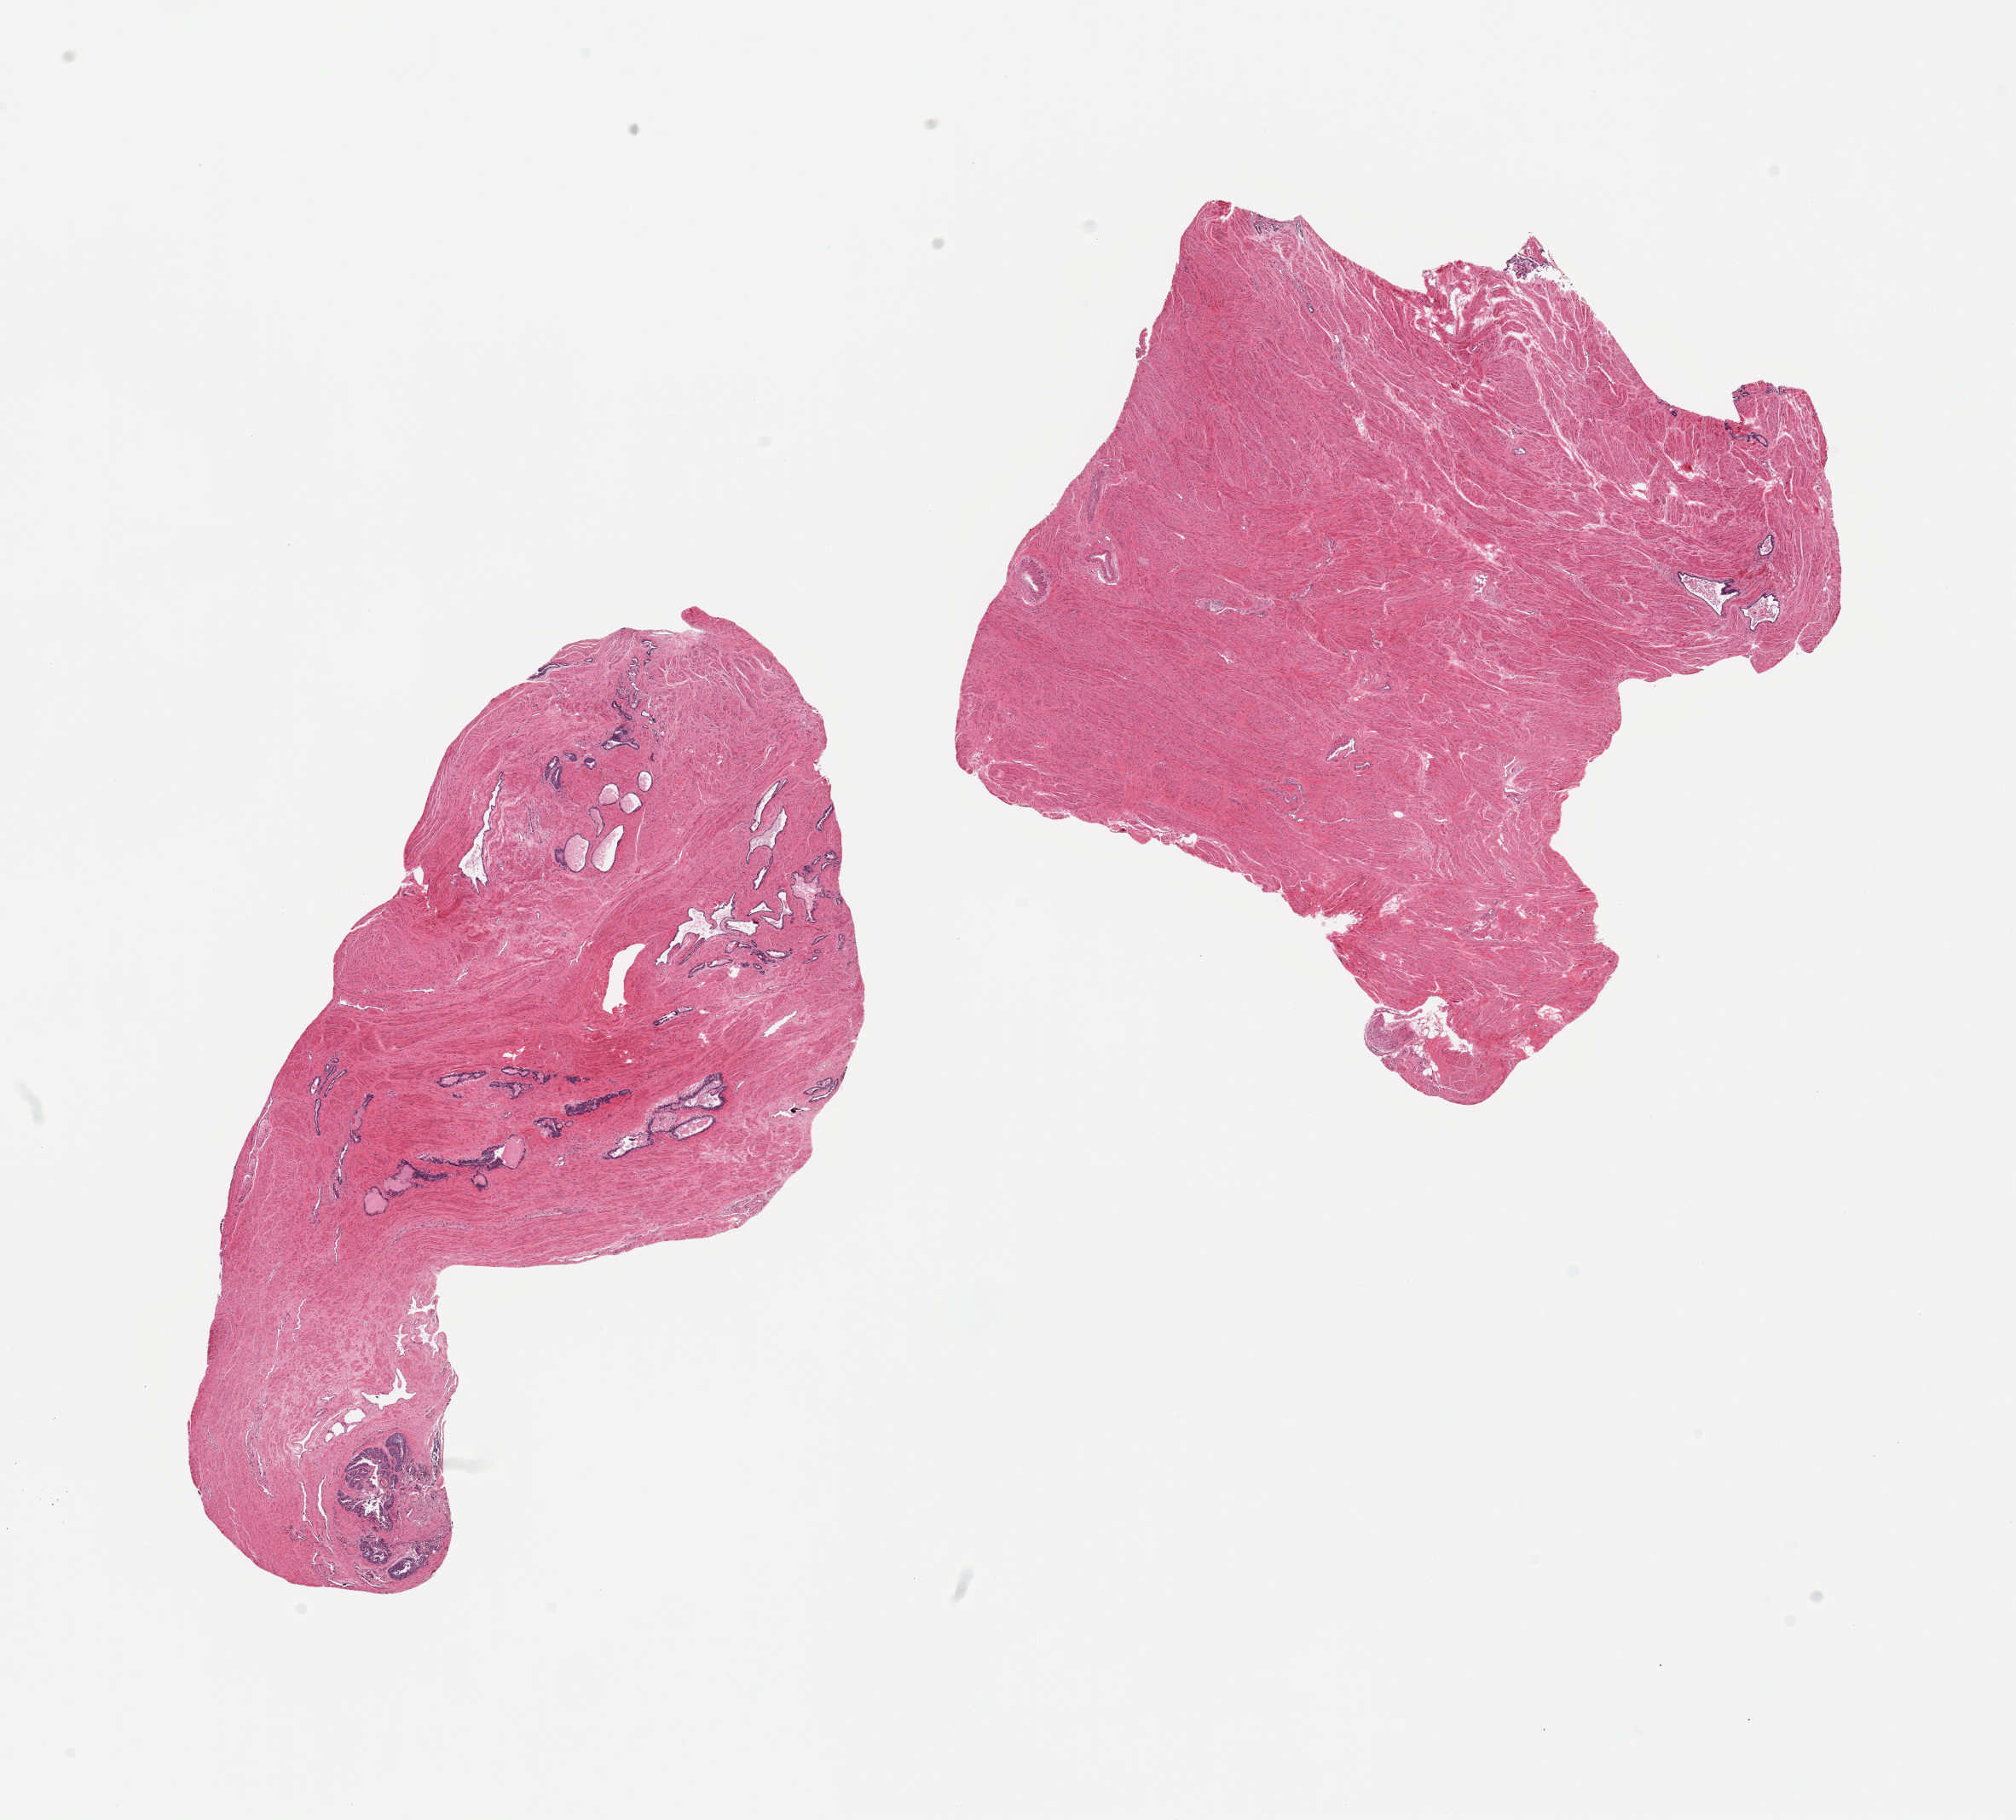
Digitized haematoxylin and eosin-stained section, shown as a low-resolution overview of the whole scanned area (about 18.7 x 16.9 mm, from a 20x scan); PAXgene-fixed, paraffin-embedded tissue; section of prostate (target tissue); donor tissue sample.
Review note (as recorded): 2 pieces, mainly stromal elements; a few well-preserved glands.